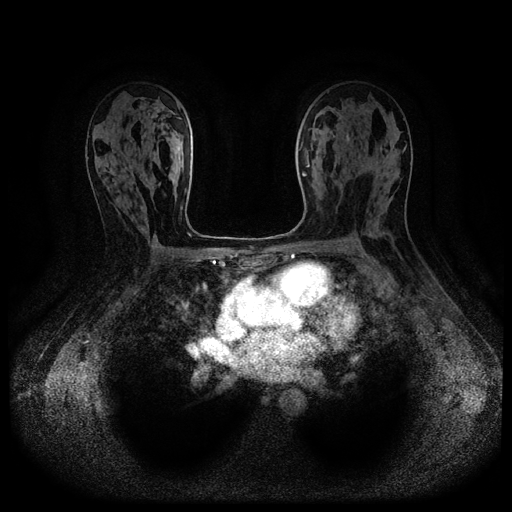
Breast MRI (dynamic contrast-enhanced, multi-phase), one axial slice; position 65 of 116 along the scan axis; dynamic contrast-enhanced series, time point 2 of 5 at this slice position (early post-contrast); 1.5 T; TE 2.6 ms, TR 5.3 ms; 2.2 mm slice thickness; 512 × 512 image matrix. Female patient, age 54 years.
Outlined on this slice (semi-automatically segmented with operator editing):
- breast lesion (labelled benign in the annotation): bounding box (x1, y1, x2, y2) in pixels: (346, 134, 350, 142)